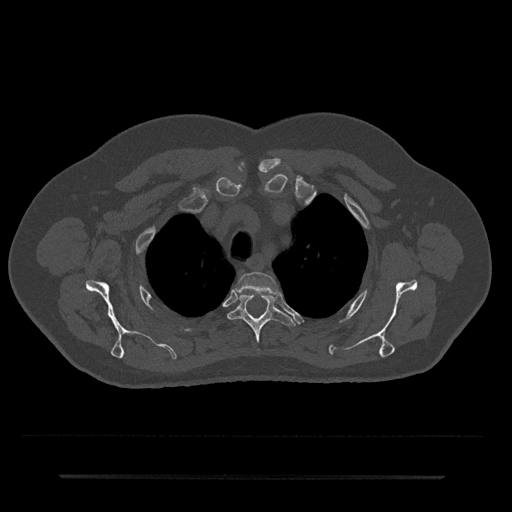
CT including the spine, one axial slice. Position 575 of 797 along the scan axis. Reconstruction kernel Br40s/3. 120 kVp. Bone window (W 1800 / L 400 HU). 0.5 mm slice thickness. 512 × 512 image matrix, field of view 437 × 437 mm. Patient: male, 69 years. From the clinical record (not read from this slice): primary cancer: prostate.
Structures marked on this image (semi-automatic segmentation, software-assisted and operator-edited):
- T2 vertebra: box from (x=236, y=272) to (x=278, y=294) px
- T3 vertebra: (x=227, y=294)–(x=296, y=351)